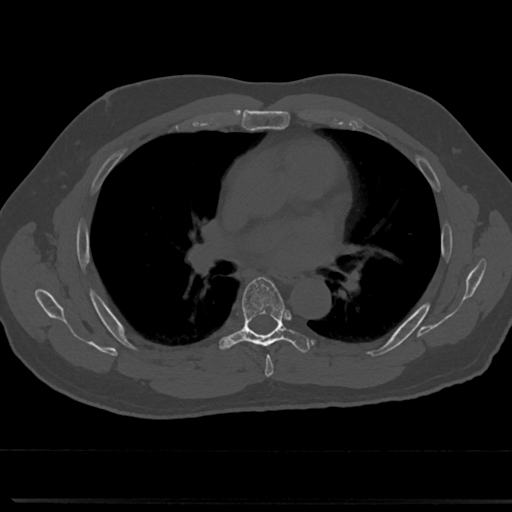
CT including the spine, one axial slice; slice 459 of 817 in the series (ordered by position); reconstruction kernel Br40s/3; 120 kVp; bone window (W 1800 / L 400 HU); 0.5 mm slice thickness; 512 × 512 image matrix. Male patient, age 61 years. Case-level facts recorded for this patient, not image findings: primary cancer: prostate.
Outlined on this slice (semi-automatic segmentation, software-assisted and operator-edited):
- T5 vertebra: box from (x=257, y=342) to (x=273, y=369) px
- T6 vertebra: (x=217, y=276)–(x=309, y=356)